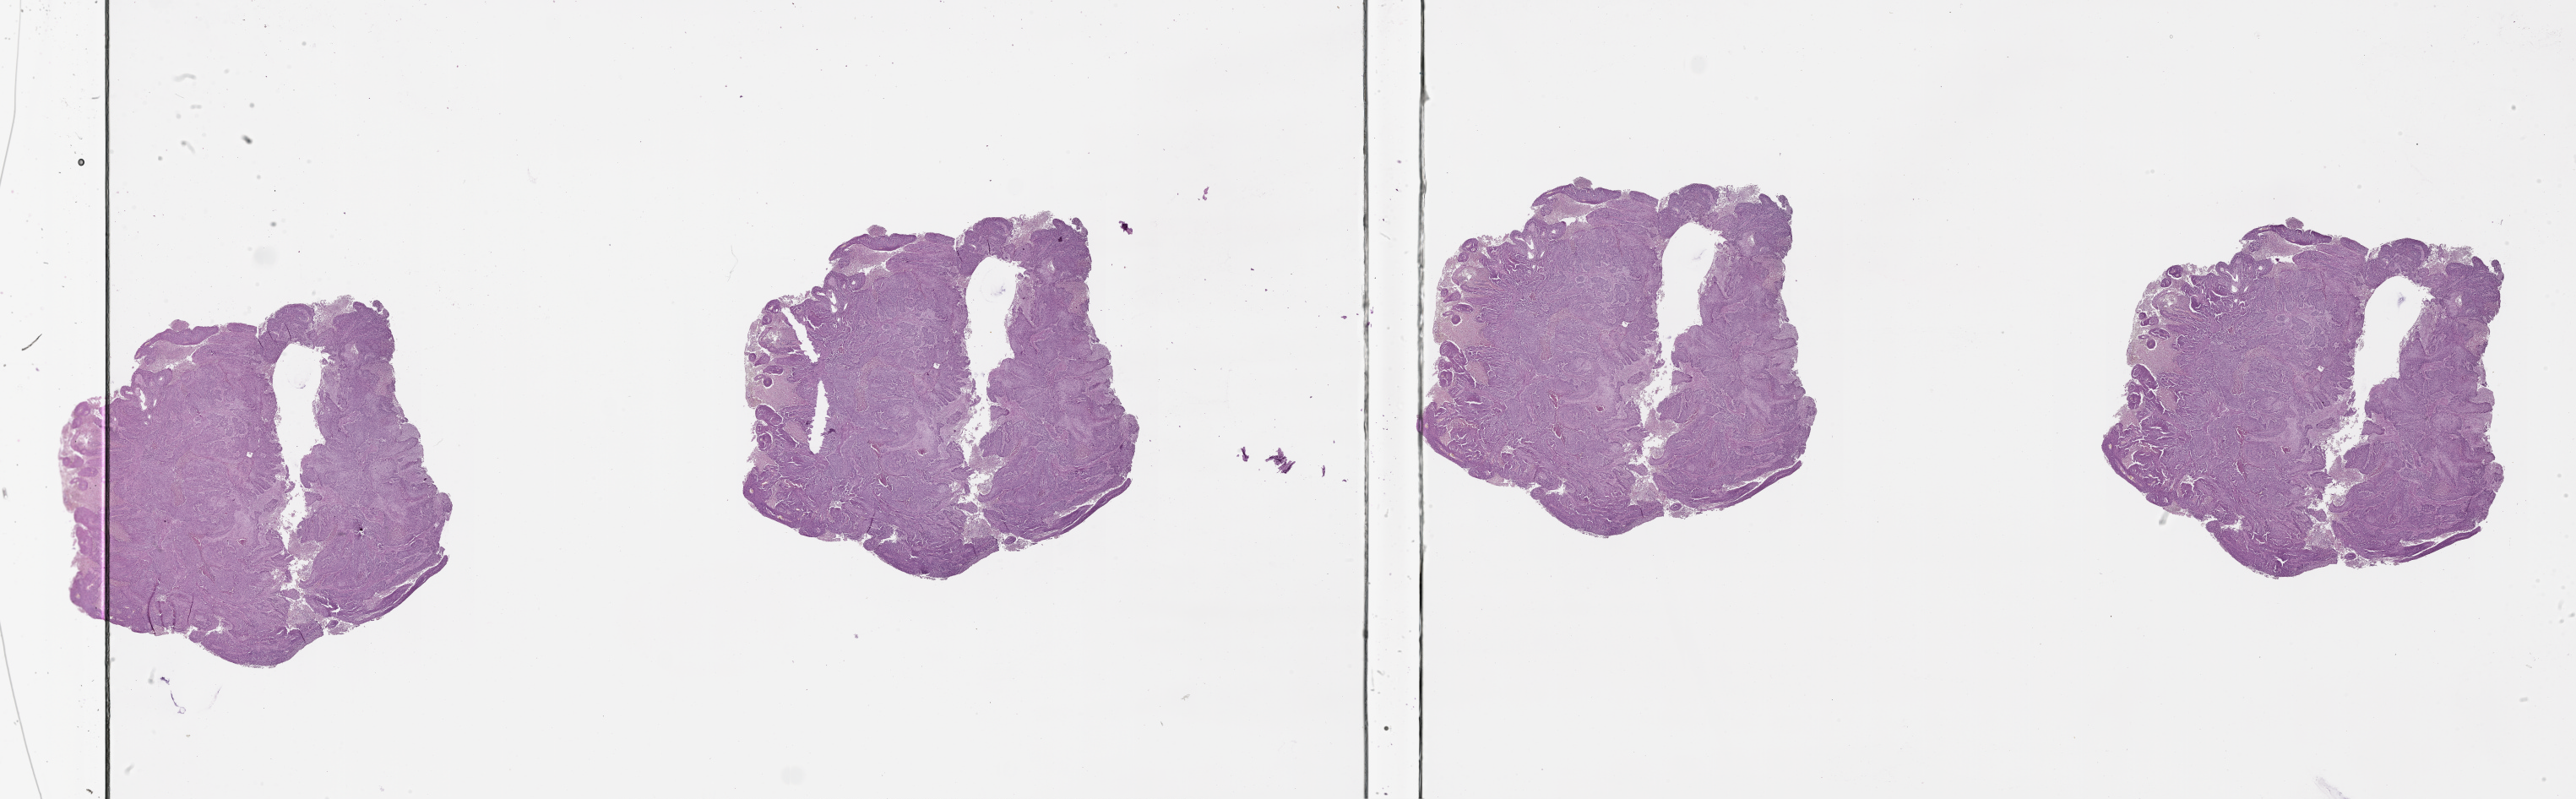
H&E-stained whole-slide image — a low-resolution overview of the entire scanned area, about 49.1 x 15.2 mm. Lung, tumour tissue. 63-year-old female patient.
• patient diagnosis (cohort enrolment): squamous cell carcinoma (lung)